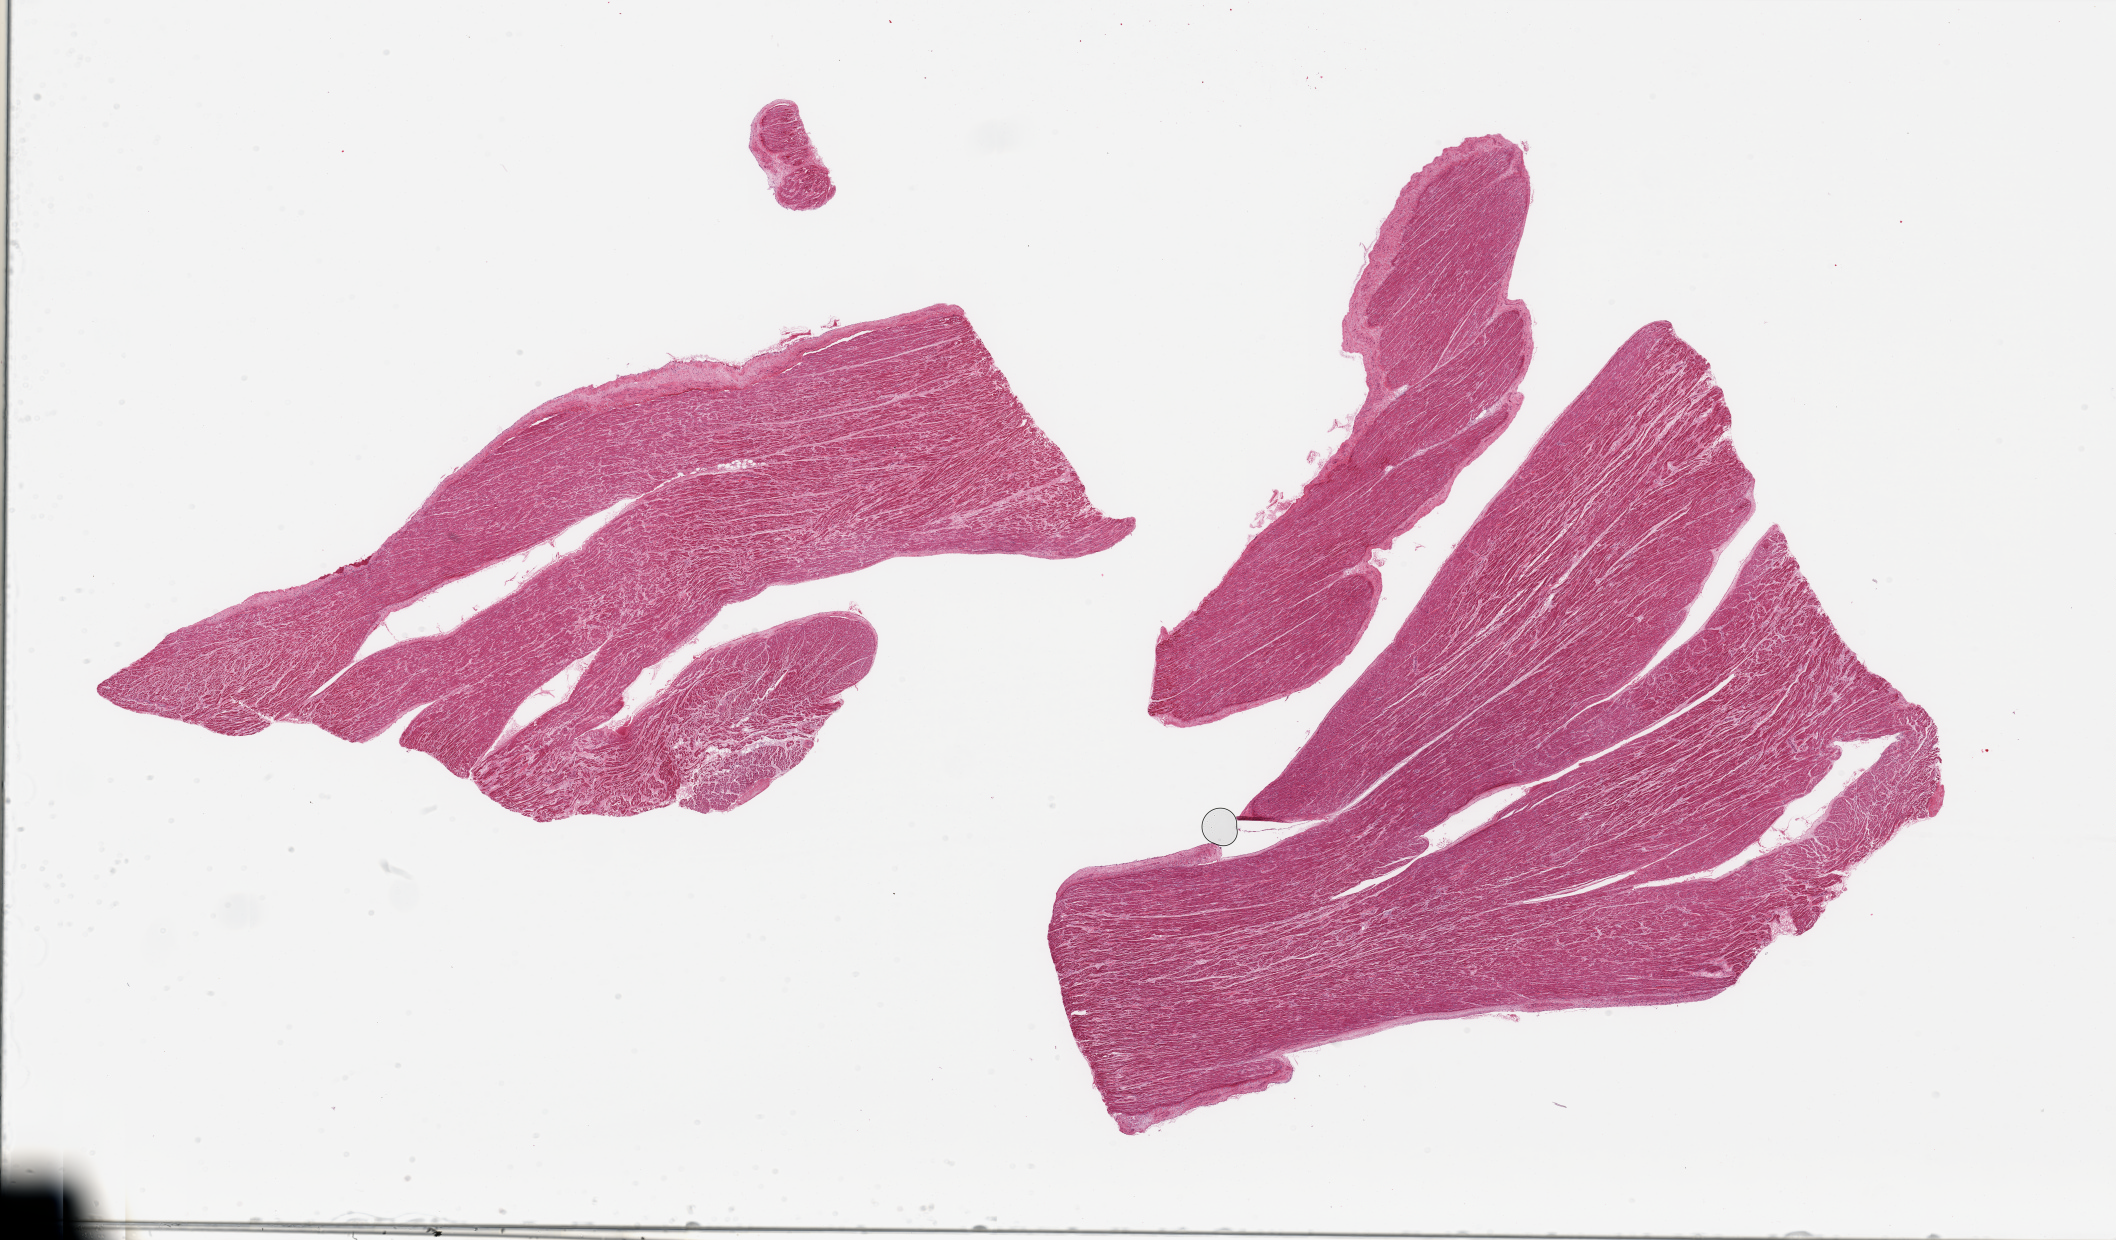
Whole-slide image, H&E stain — shown as a low-resolution overview of the whole scanned area (about 33.5 x 19.6 mm), PAXgene-fixed paraffin-embedded (PFPE) section, target tissue: auricular appendage, donor tissue sample. Donor: female.
• pathologist's review note for this sample: 2 pieces; no fat and <1% fibrous content